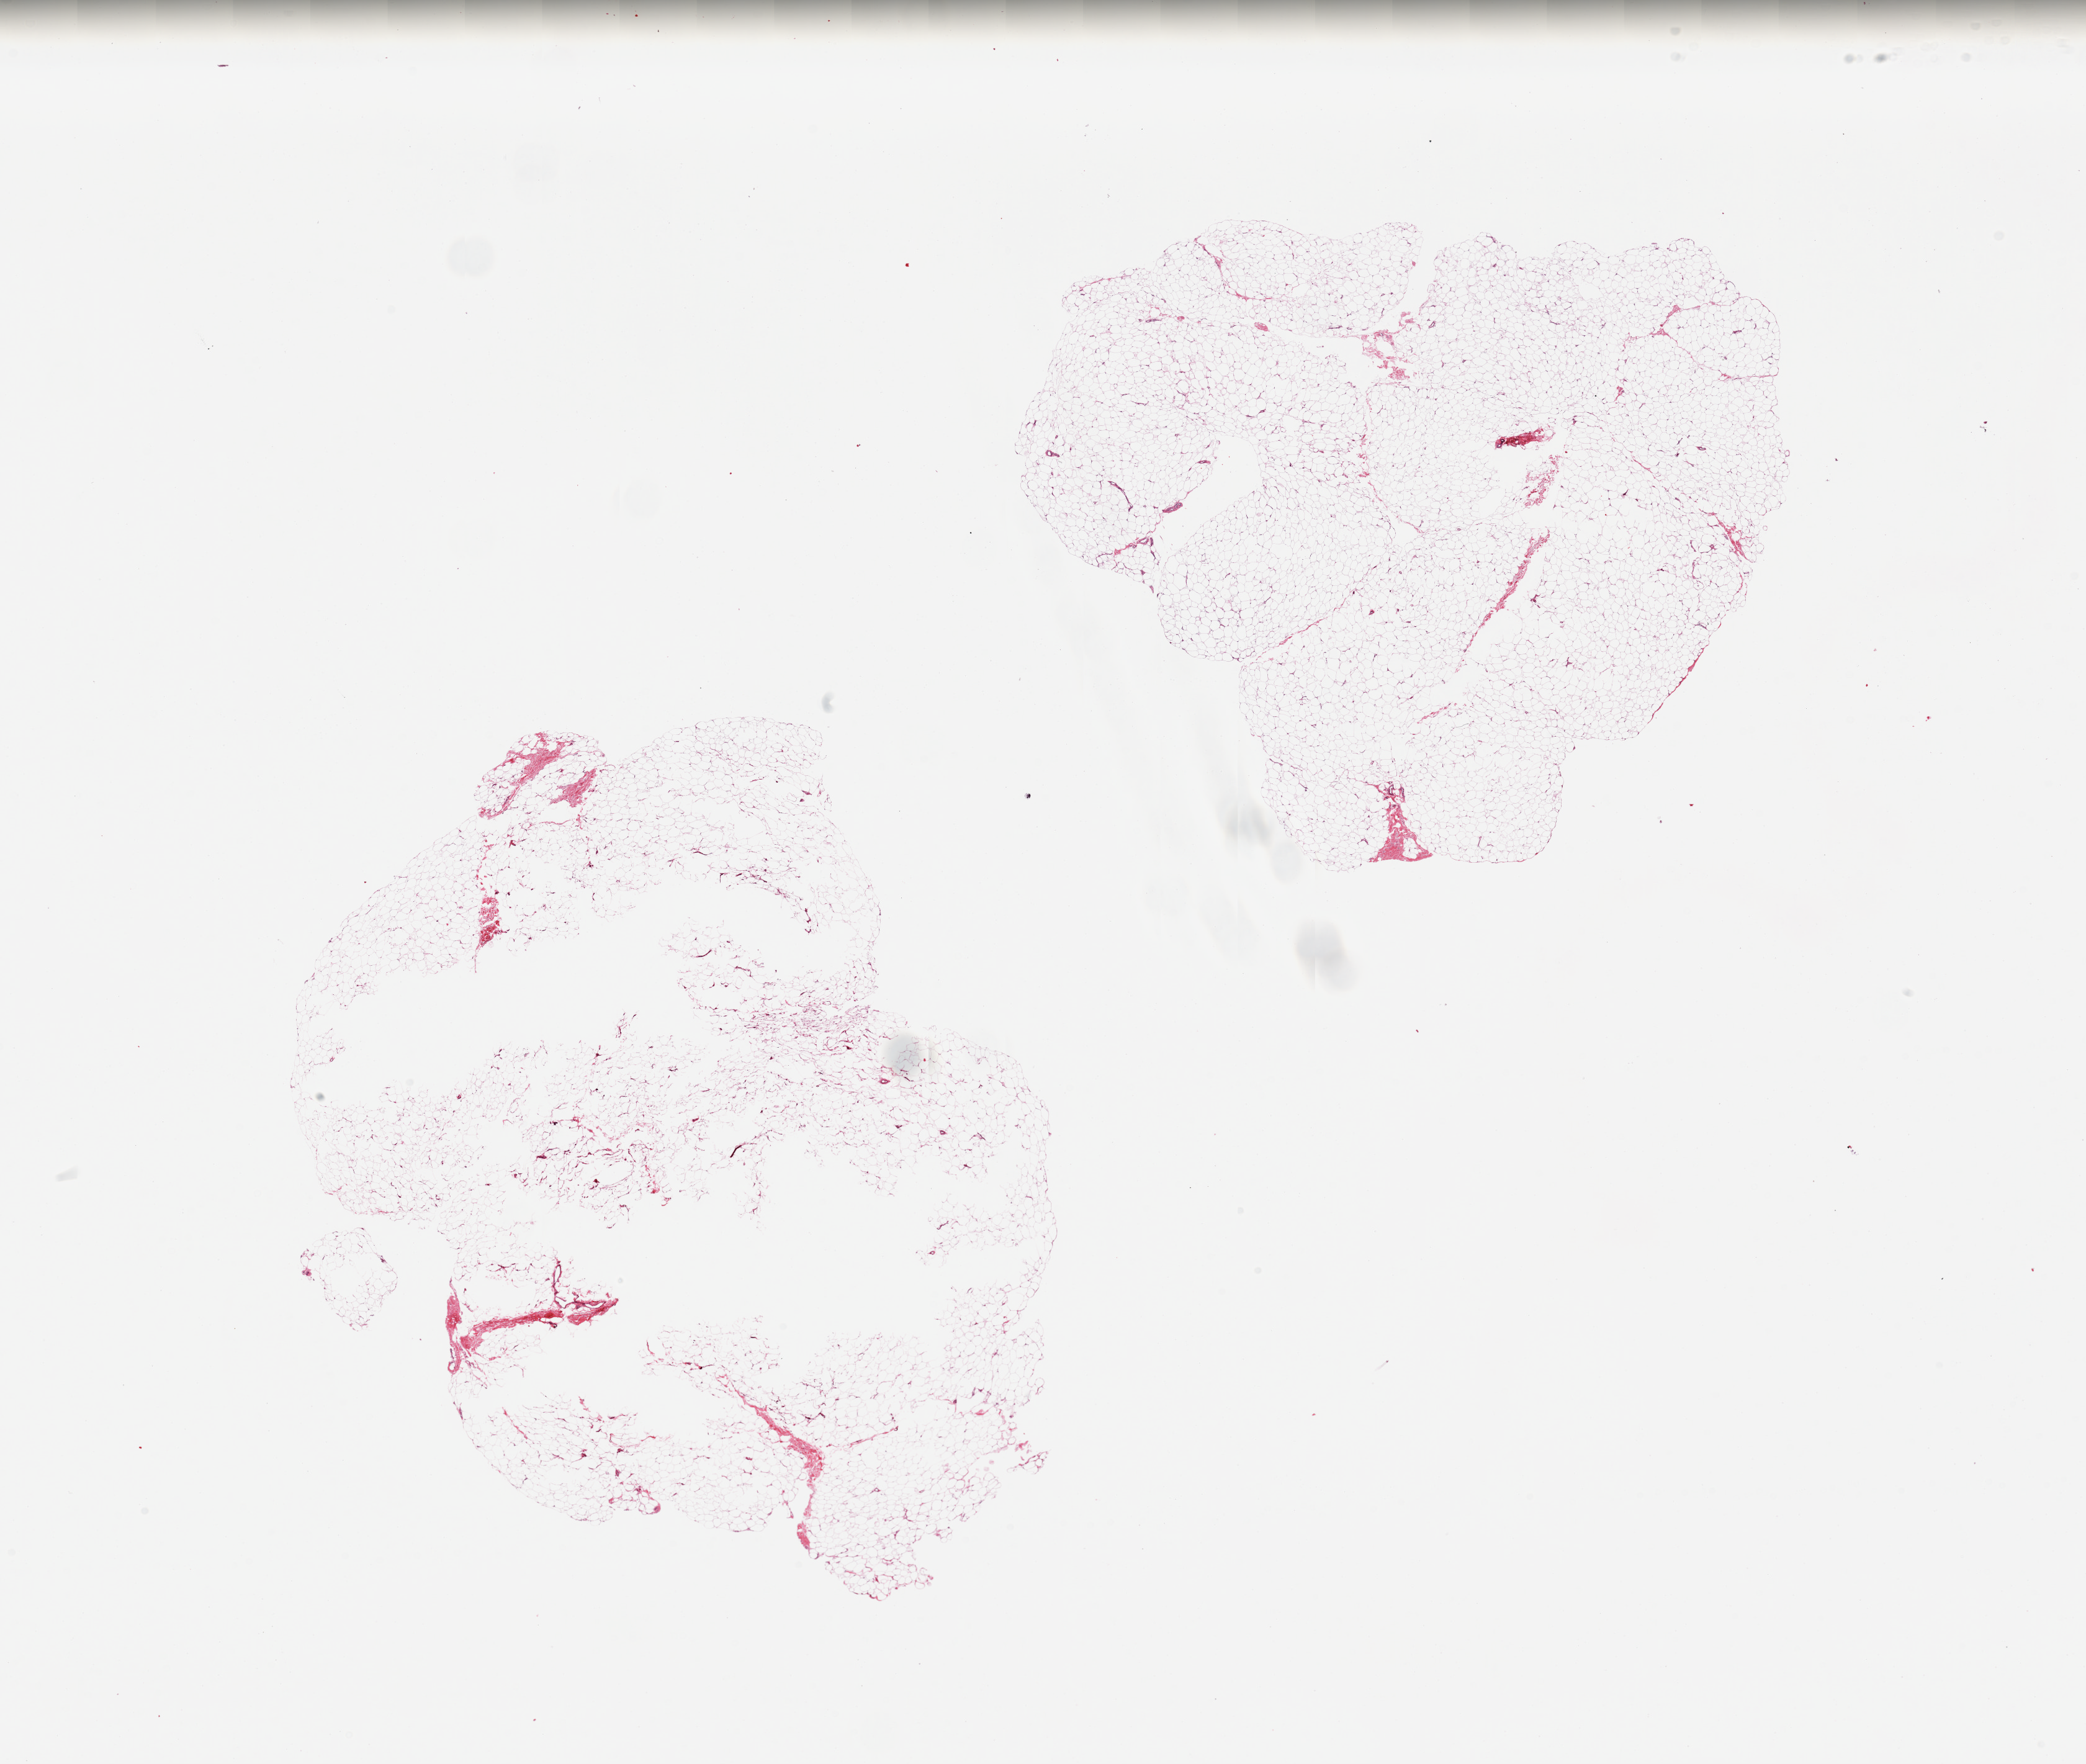
Whole-slide image, haematoxylin and eosin stain, low-resolution overview of the scanned area, about 26.6 x 22.5 mm (from a 20x scan), PAXgene-fixed, paraffin-embedded tissue, target tissue: adipose tissue, donor tissue sample. Donor sex: female.
Pathologist's review note for this sample: 2 pieces, minimal fibrous tissue, <~2%.